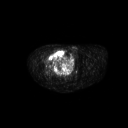
FDG PET of an extremity soft-tissue mass (from a PET/CT study), one axial slice. Position 271 of 311 along the scan axis. 3.27 mm slice thickness. 128 × 128 image matrix, field of view 700 × 700 mm. Patient: male, 50 years. From the clinical record (not read from this slice): histological type: undifferentiated - pleiomorphic; grade: high; site of the primary tumour: right thigh.
Structures marked on this image (expert contour drawn on MRI and transferred to this co-registered scan by the dataset authors):
- gross tumour volume including surrounding oedema: bounding box (x1, y1, x2, y2) in pixels: (46, 49, 66, 68)
- gross tumour volume (mass): (46, 49, 66, 68)